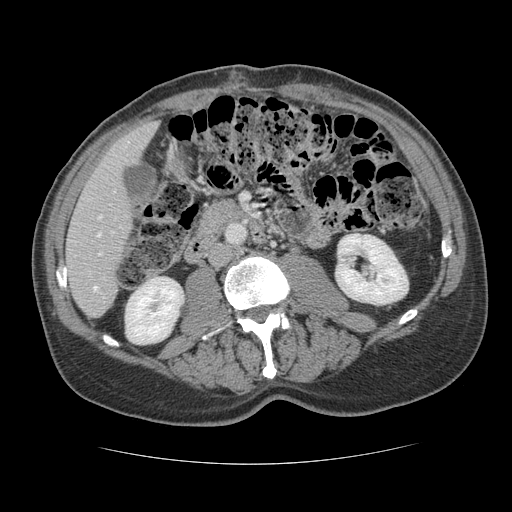
Contrast-enhanced abdominal CT, one axial slice. Position 43 of 134 along the scan axis. Reconstruction kernel STANDARD. Intravenous contrast given. Soft-tissue window (W 400 / L 40 HU). 512 × 512 image matrix, field of view 377 × 377 mm. Male patient, age 68 years. From the clinical record (not read from this slice): diagnosis: colorectal cancer liver metastases, imaged before liver resection; multiple liver metastases: yes; largest metastasis: 2.2 cm; disease in both lobes: no.
Outlined on this slice (manually delineated by an expert):
- hepatic veins: box from (x=97, y=216) to (x=101, y=237) px
- liver: (x=66, y=122)–(x=156, y=317)
- planned liver remnant (the part of the liver to remain after resection): (x=66, y=122)–(x=156, y=317)
- portal vein (with intrahepatic branches): (x=93, y=253)–(x=101, y=290)